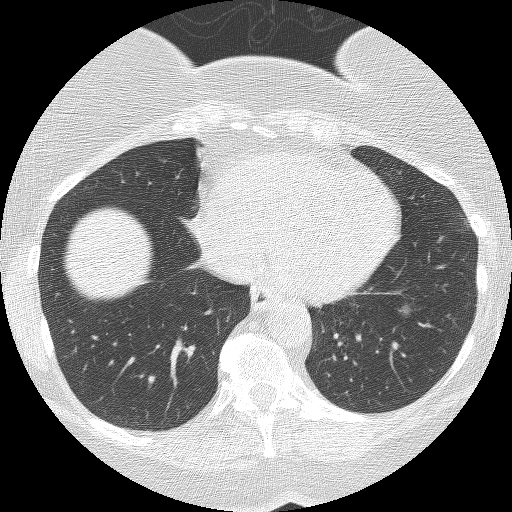
Chest CT (low-dose screening protocol), one axial image; third annual screen; lung window (W 1500 / L -600 HU); 2.5 mm slice thickness; slice 113 of 167 in the series; 512 × 512 image matrix, field of view 300 × 300 mm. Female participant, aged 55 years at enrolment. Former smoker at enrolment.
Expert reader's lesion annotation, bounding box (x1, y1, x2, y2) in pixels: (378, 292, 429, 338). The screening reader recorded 3 non-calcified nodules or masses ≥4 mm on this exam (right lower lobe, right lower lobe, left lower lobe); which of them this box marks is not recorded.